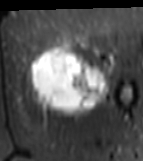
MRI of an extremity soft-tissue mass, one axial slice. Slice 23 of 81 in the series (ordered by position). STIR. MR volume resampled by the dataset authors to the PET/CT grid (not the native acquisition matrix). 3.27 mm slice thickness. 143 × 161 image matrix, field of view 140 × 157 mm. Female patient. From the clinical record (not read from this slice): histological type: myxofibrosarcoma; grade: intermediate; site of the primary tumour: left thigh.
Outlined on this slice (expert contour drawn on MRI and transferred to this co-registered scan by the dataset authors):
- gross tumour volume including surrounding oedema: bounding box <28,42,114,116> (left, top, right, bottom; pixels)
- gross tumour volume (mass): <29,46,112,111>